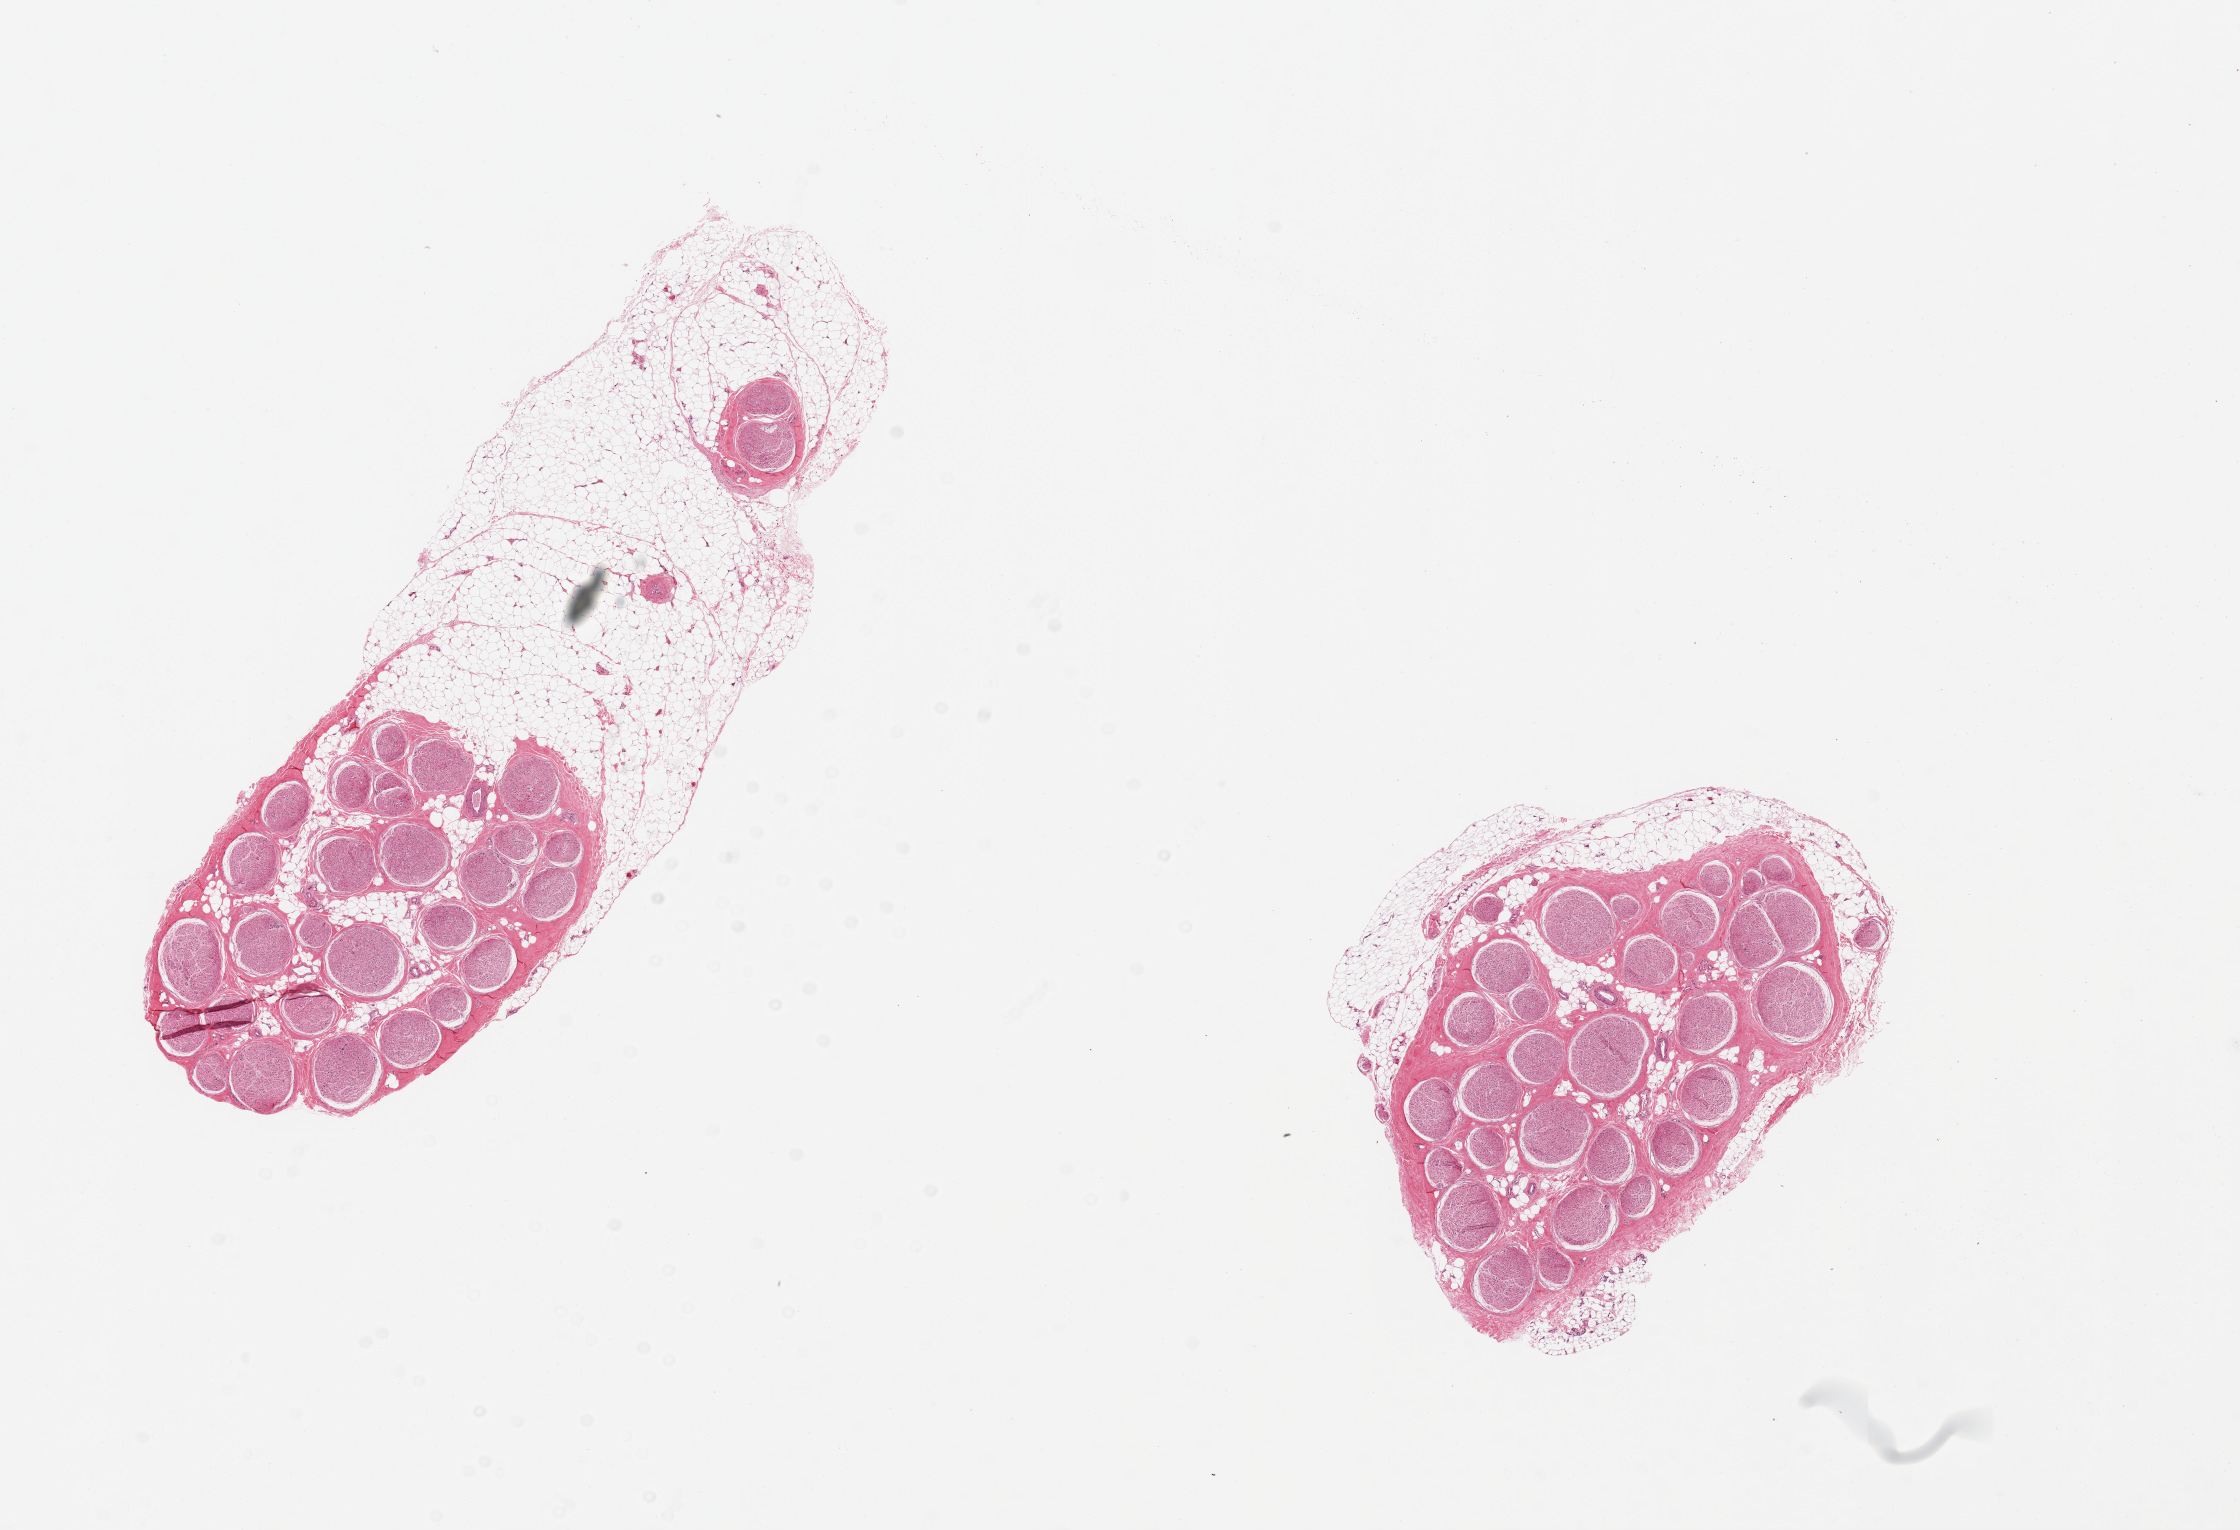
Hematoxylin and eosin (H&E) whole-slide image, brightfield, shown as a low-resolution overview of the whole scanned area (about 17.7 x 12.1 mm, acquisition: 20x scan). PAXgene-fixed, paraffin-embedded tissue. Sampled site (target tissue): tibial nerve. Donor tissue sample. Donor: male.
Review note (as recorded): 2 pieces ~ 3.5mm. Adherent fat nubbin ~5x3mm on one; rim of fat ~0.5mm on the other.